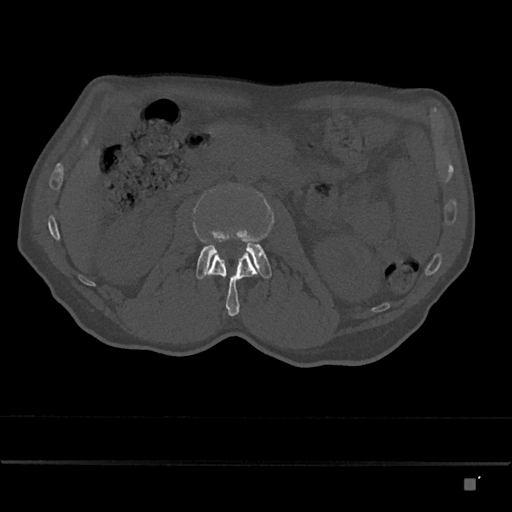
CT including the spine, one axial slice. Position 442 of 797 along the scan axis. Reconstruction kernel Br40s/3. 120 kVp. Bone window (W 1800 / L 400 HU). 0.5 mm slice thickness. 512 × 512 image matrix, field of view 390 × 390 mm. Patient: male, 72 years. From the clinical record (not read from this slice): primary cancer: prostate.
Outlined on this slice (semi-automatic segmentation, software-assisted and operator-edited):
- L2 vertebra: box from (x=205, y=250) to (x=257, y=317) px
- L3 vertebra: (x=196, y=231)–(x=272, y=280)